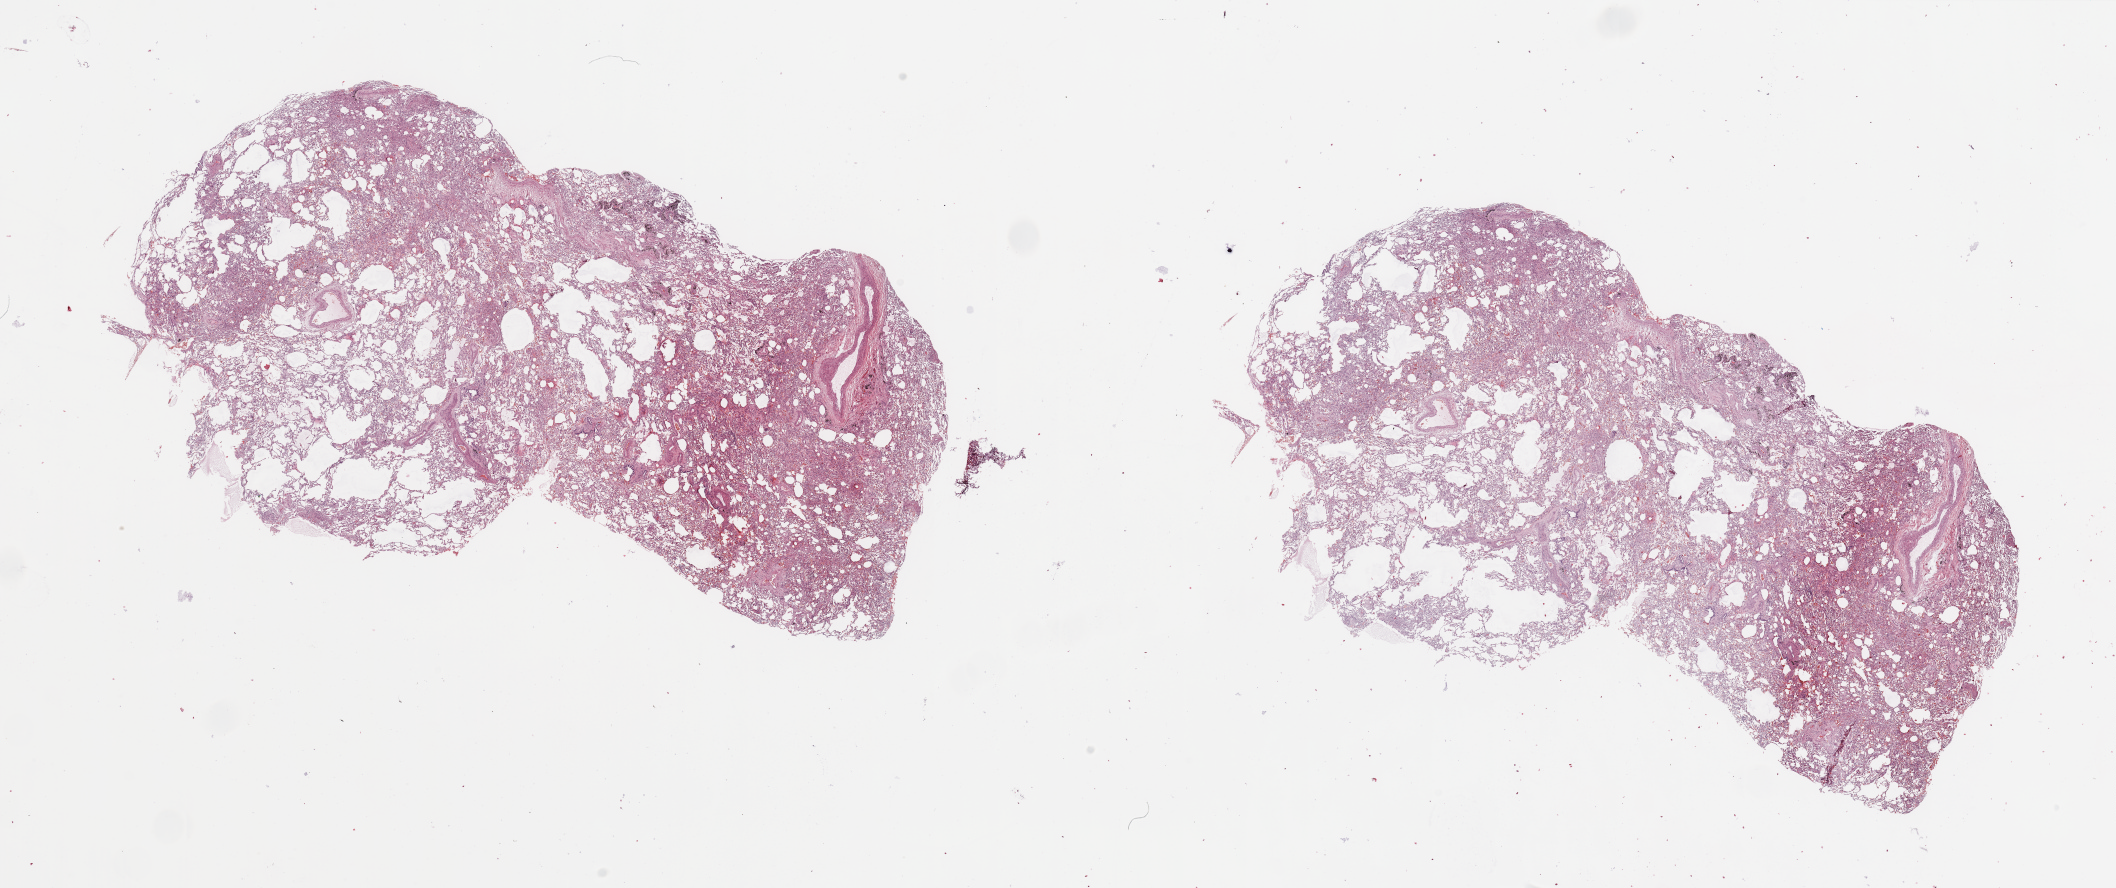
Digitized H&E tissue section (whole slide), low-resolution overview of the scanned area, about 33.5 x 14.0 mm (acquisition: 20x scan); normal (non-tumour) tissue sample, lung. 67-year-old female patient.
This section: normal (non-tumour) tissue from the same patient. Patient diagnosis: Adenocarcinoma, NOS.